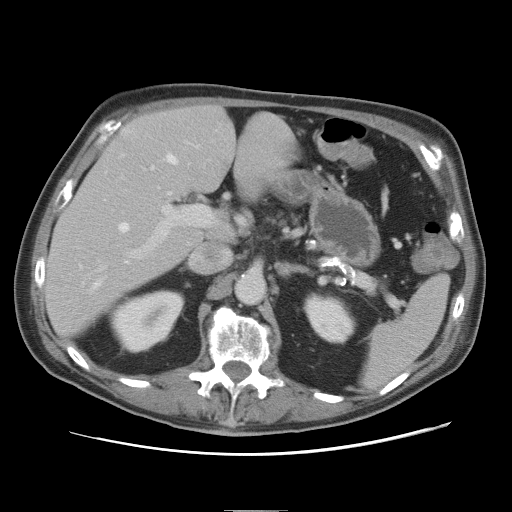
Contrast-enhanced abdominal CT, one axial slice. 120 kVp. Intravenous contrast given. Soft-tissue window (W 400 / L 40 HU). 5 mm slice thickness. 512 × 512 image matrix, field of view 375 × 375 mm. Male patient, age 69 years. From the clinical record (not read from this slice): diagnosis: colorectal cancer liver metastases, imaged before liver resection; multiple liver metastases: no; largest metastasis: 8.5 cm; disease in both lobes: no.
Structures marked on this image (outlined manually by an expert reader):
- hepatic veins: bounding box (x1, y1, x2, y2) in pixels: (94, 154, 178, 287)
- liver: (45, 108, 294, 335)
- planned liver remnant (the part of the liver to remain after resection): (45, 108, 236, 335)
- portal vein (with intrahepatic branches): (100, 166, 214, 269)